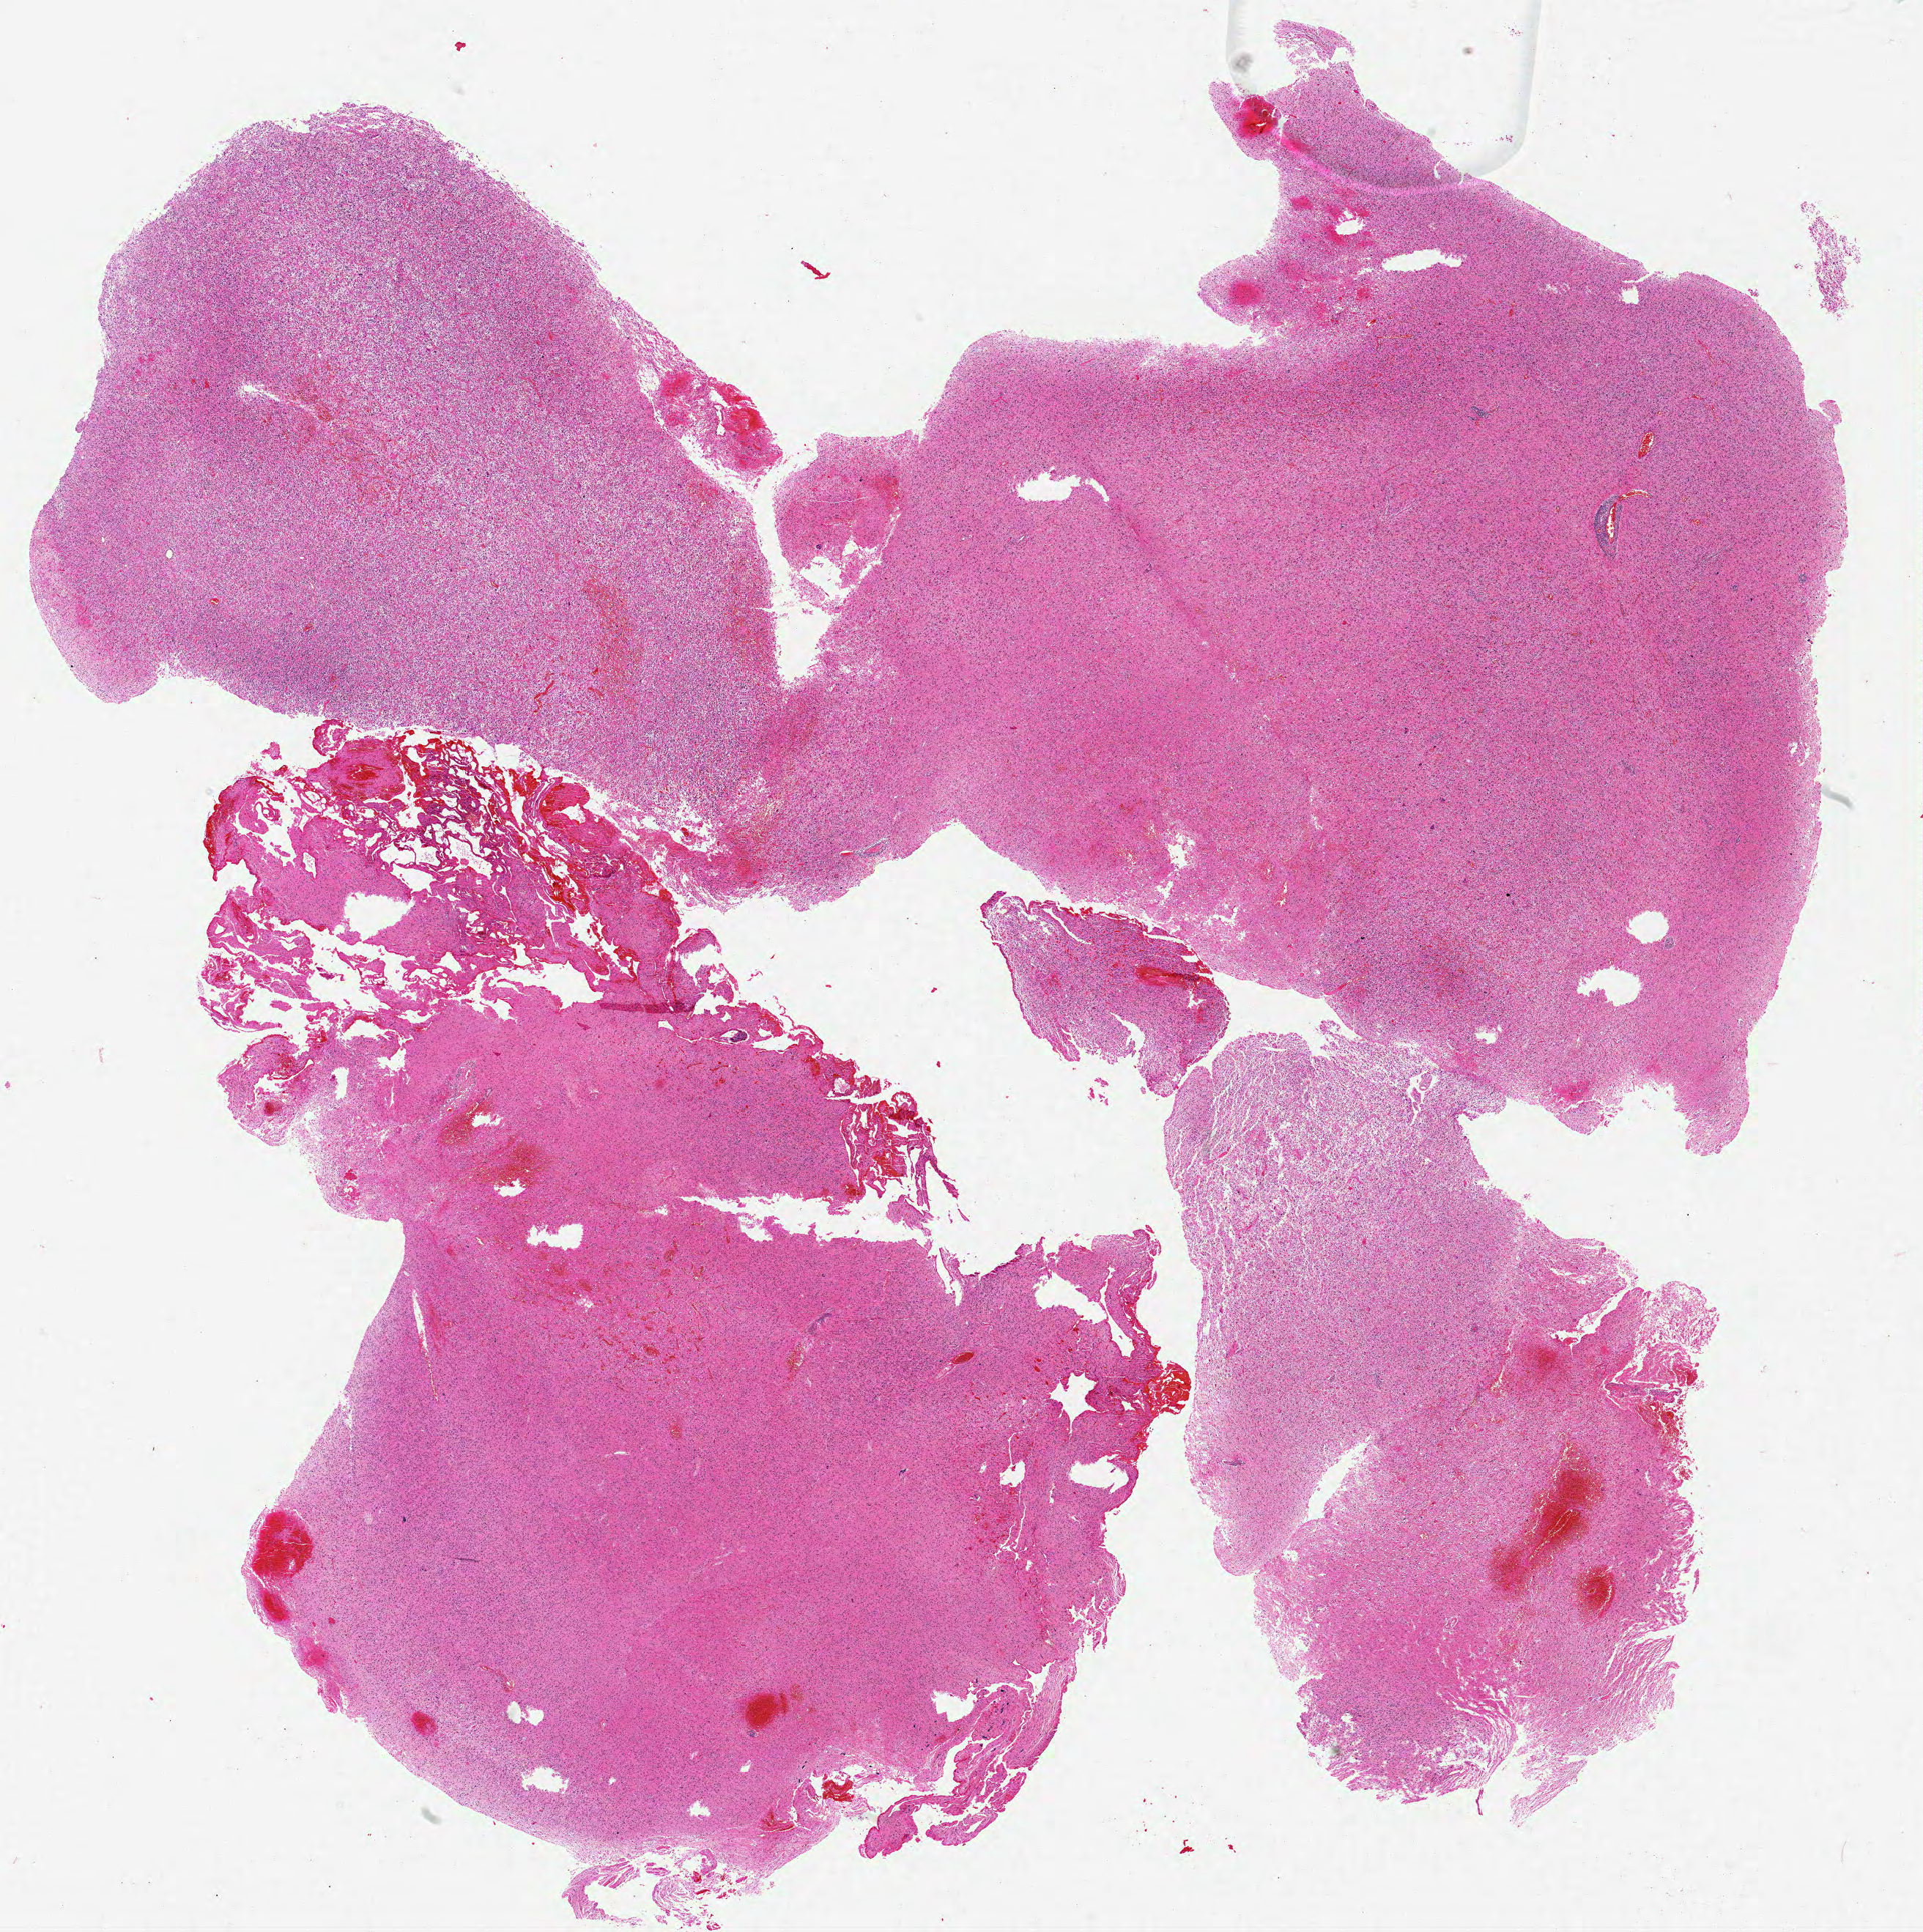
Whole-slide histology image, H&E-stained, low-resolution overview of the scanned area, about 21.0 x 21.1 mm (from a 20x scan); formalin-fixed paraffin-embedded (FFPE) diagnostic section; brain, primary tumour sample. Female, age 36 years at initial diagnosis.
Diagnosis: Glioblastoma.